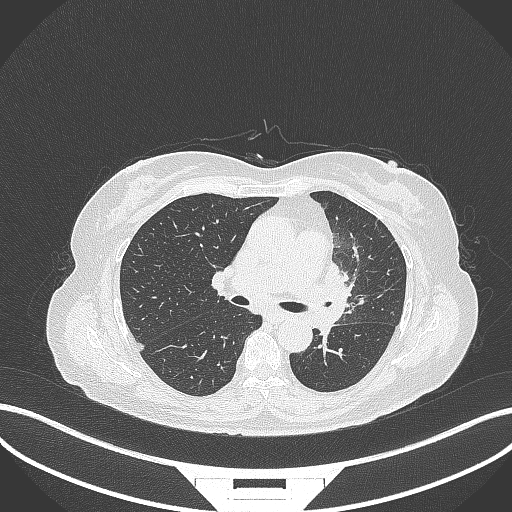
Chest CT, one axial slice. Position 197 of 382 along the scan axis. Reconstruction kernel B70f. 120 kVp. Lung window (W 1500 / L -600 HU). 512 × 512 image matrix, field of view 400 × 400 mm. Female patient, age 64 years. From the clinical record (not read from this slice): clinical TNM (as recorded): T2a N2 M0.
Annotated regions visible in this slice (rectangle marked by the reading radiologist):
- lung tumour (recorded histology: adenocarcinoma): bounding box [x1, y1, x2, y2] px = [315, 255, 356, 336]